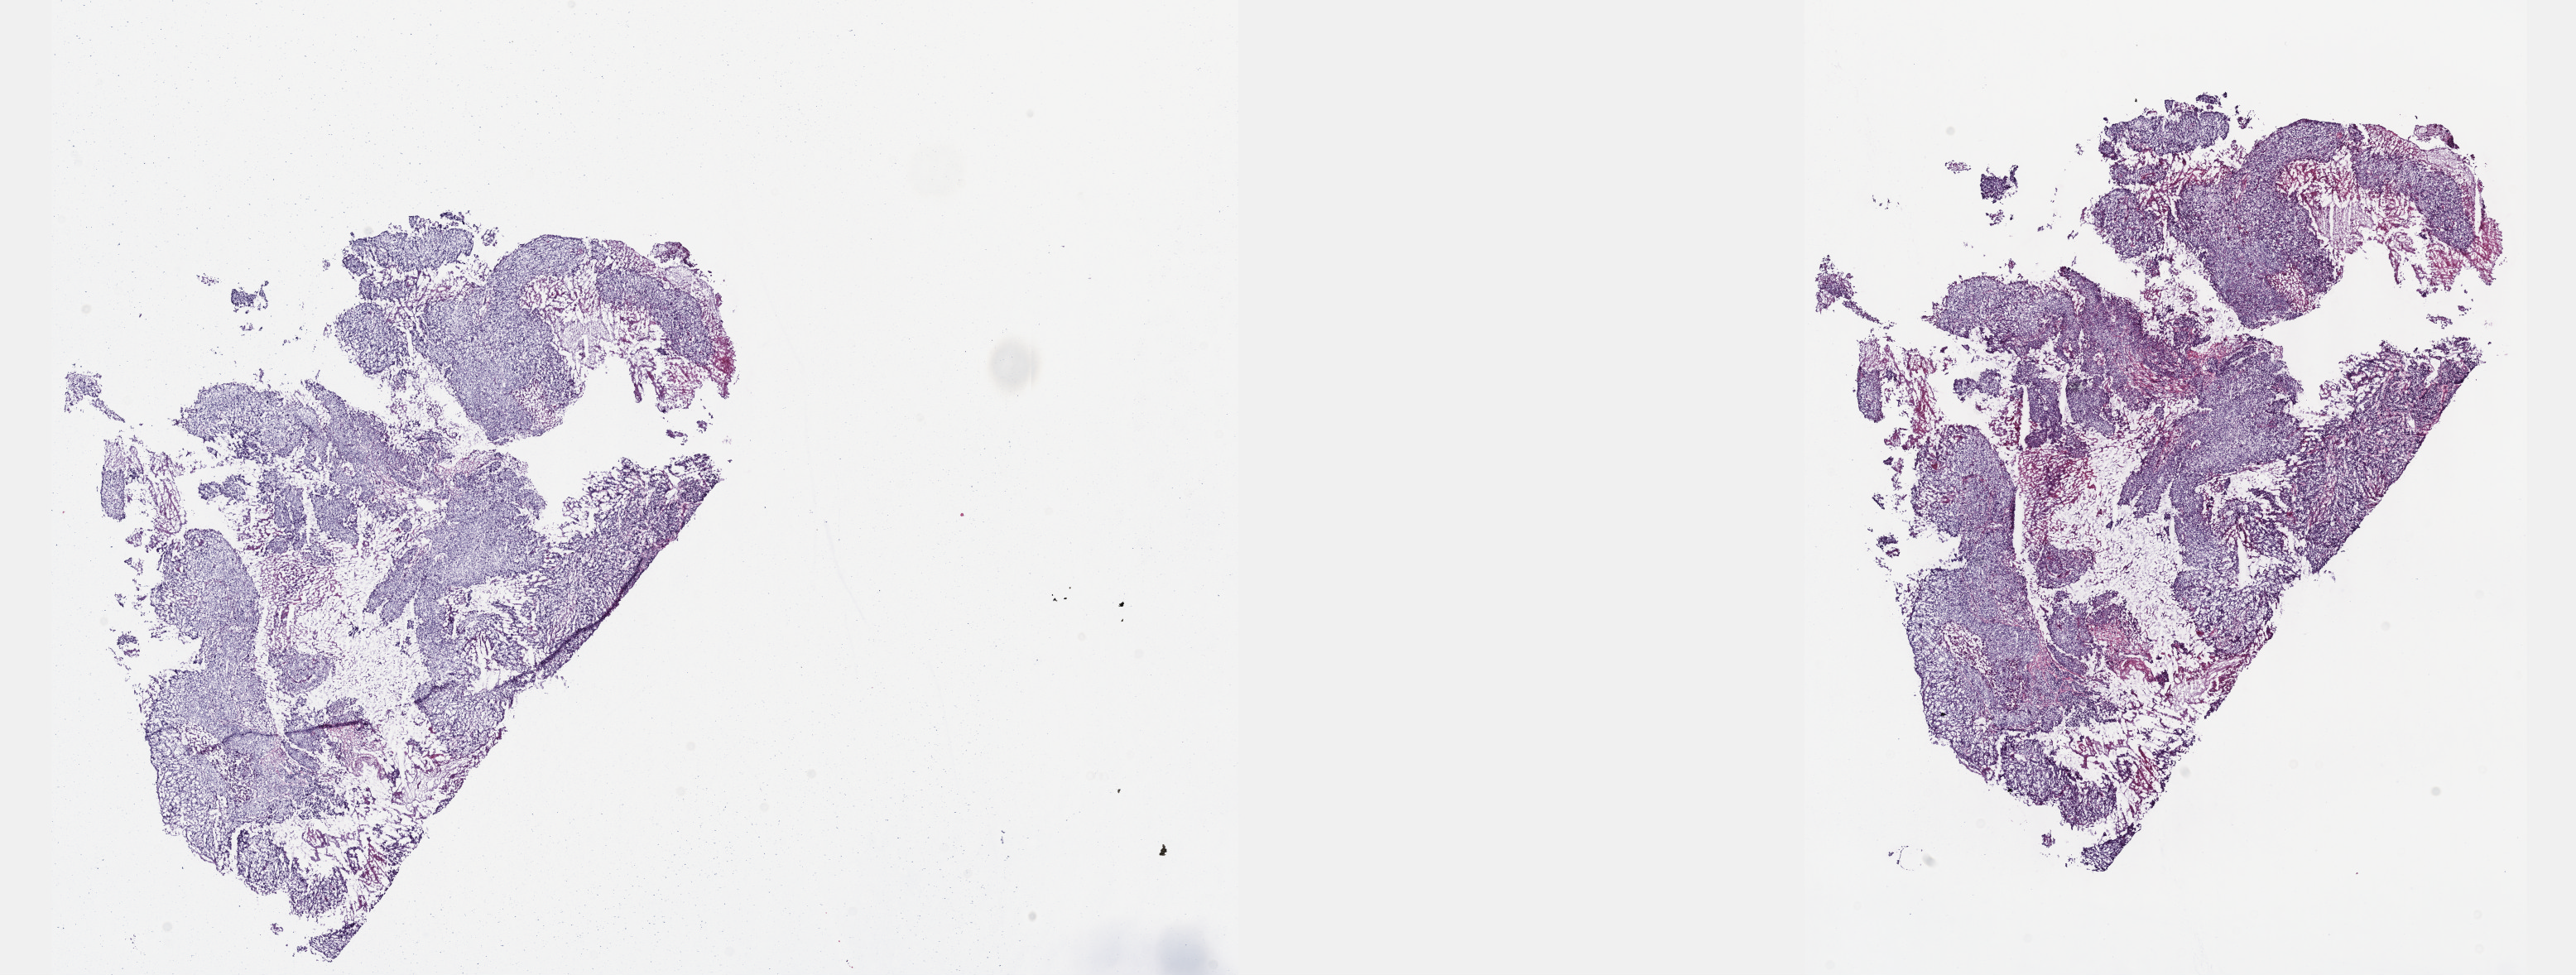
Whole-slide histology image, Hematoxylin and eosin (H&E) stained — whole scanned area (about 25.1 x 9.5 mm) shown as a low-resolution overview, frozen section, sample: primary tumour, cervix. Female, age 34 years at initial diagnosis.
Pathologic diagnosis: Squamous cell carcinoma, large cell, nonkeratinizing, NOS (cervix uteri).